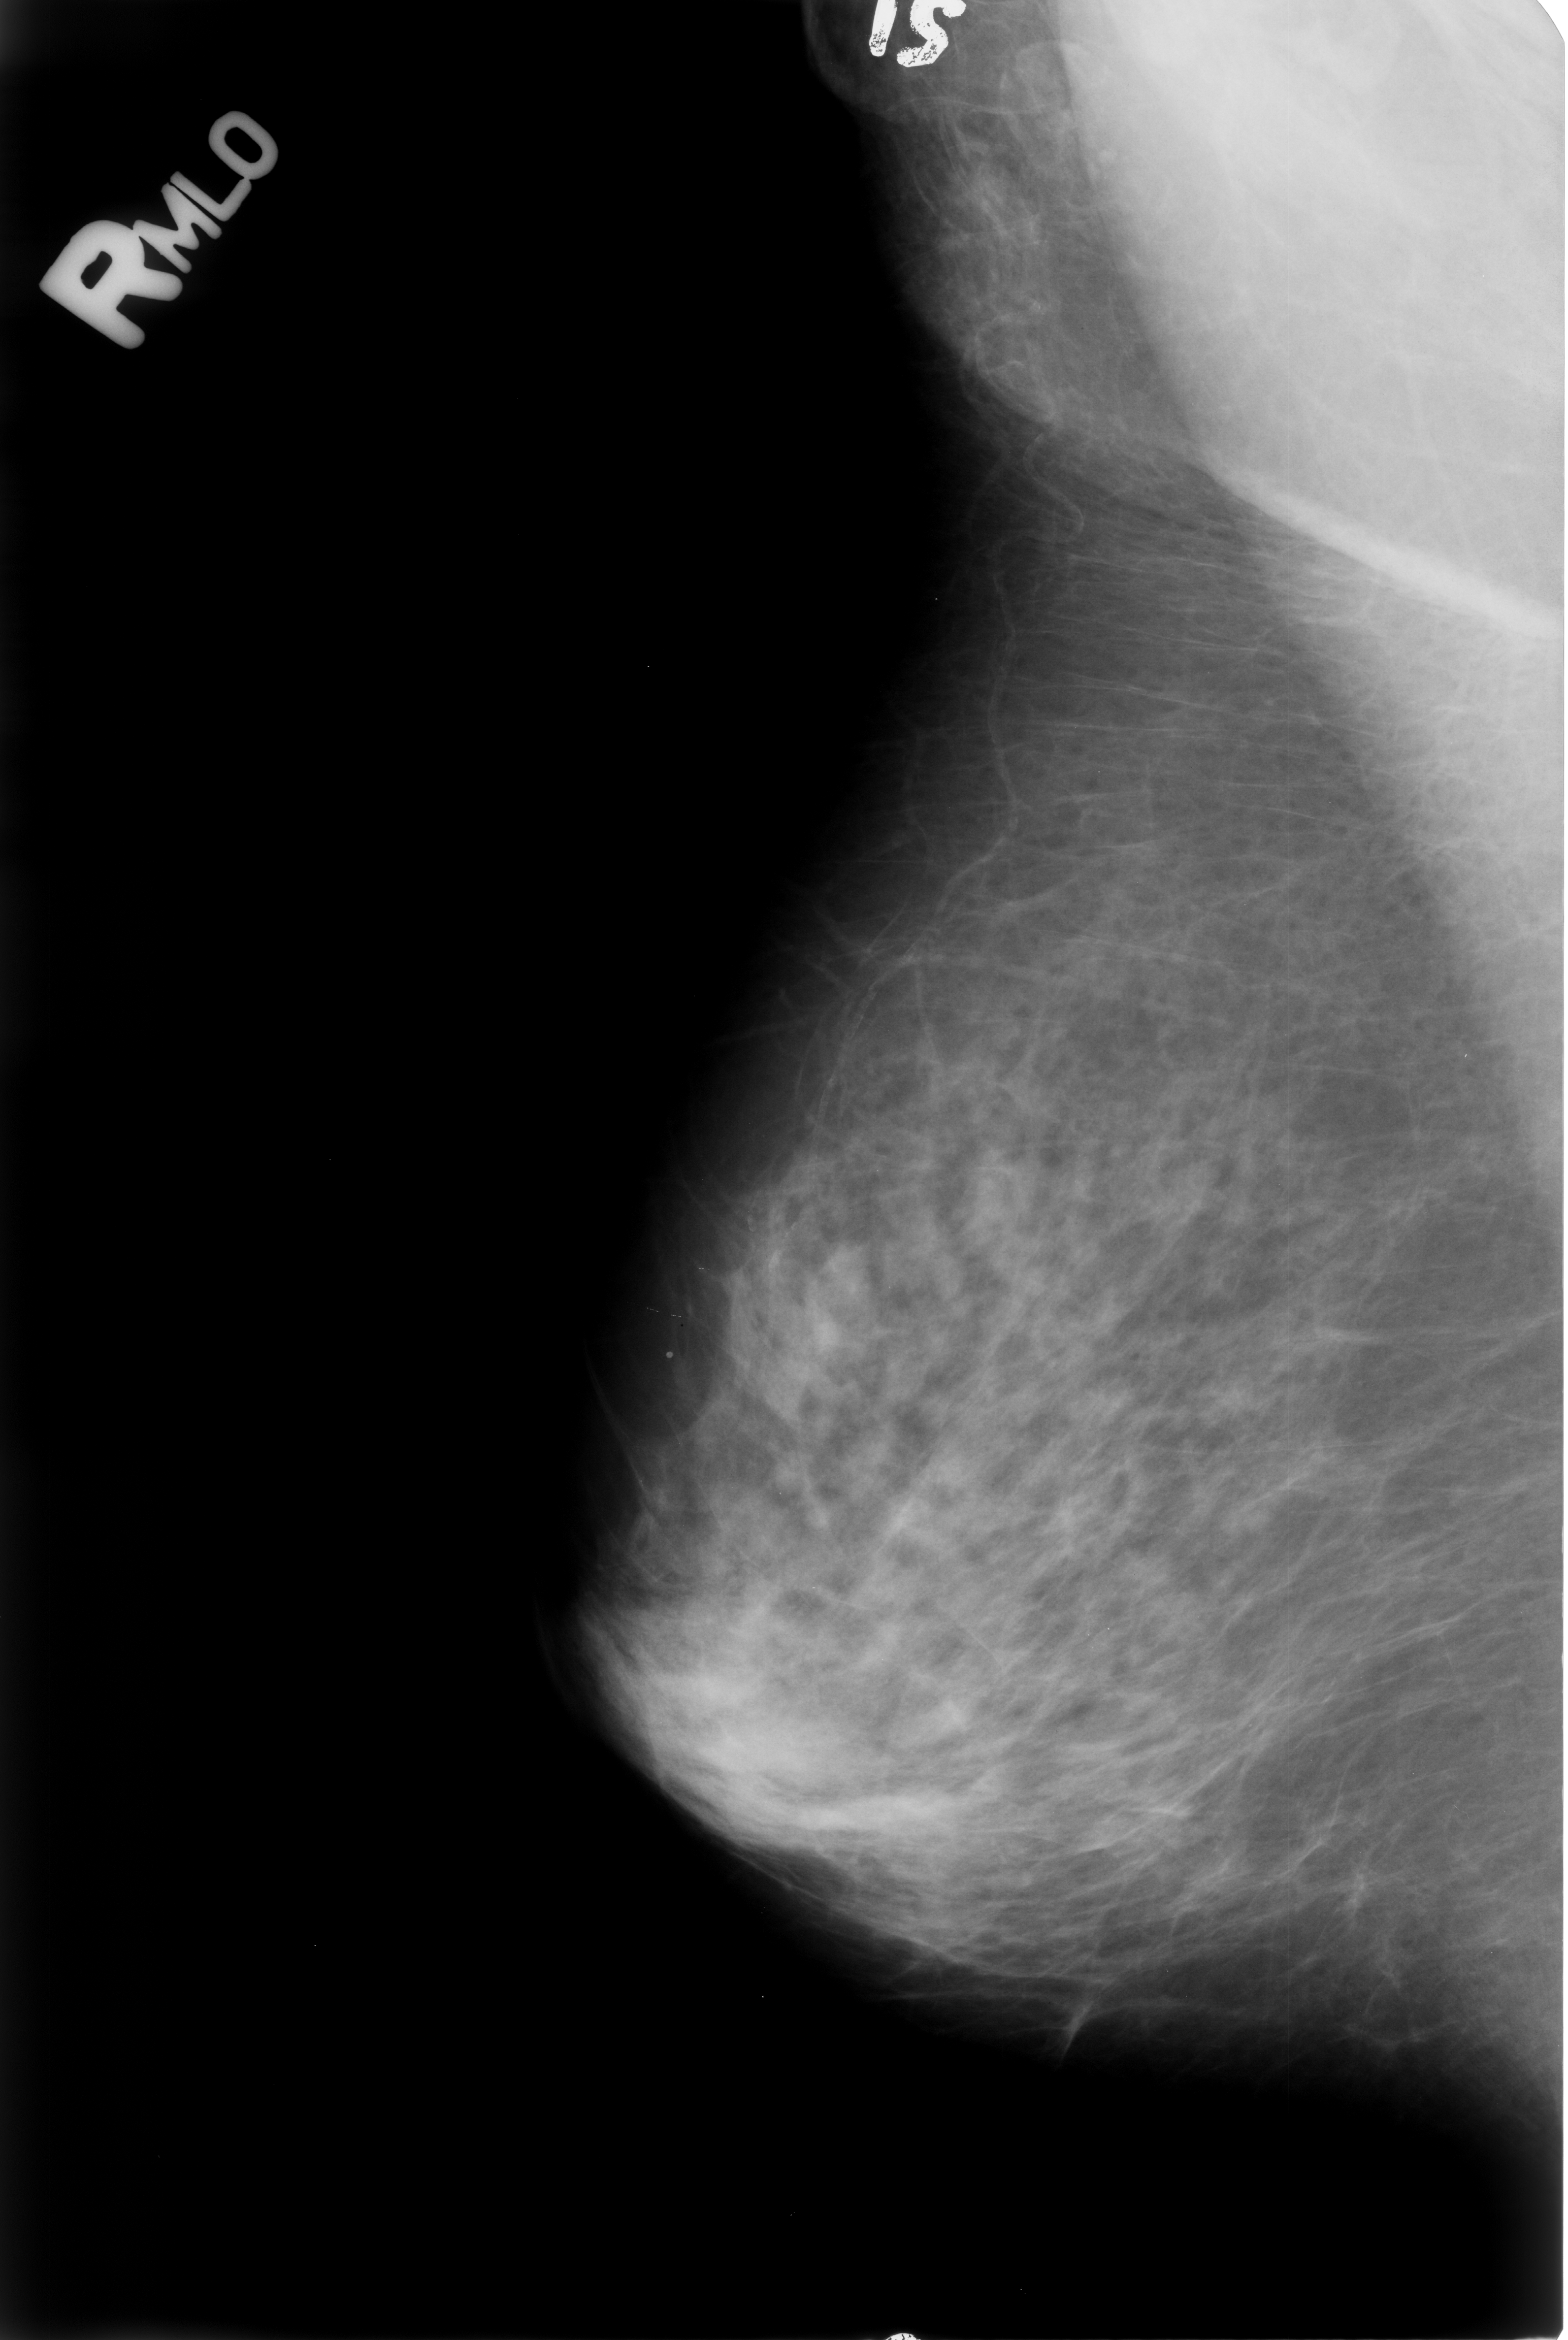
Digitized screen-film mammogram. Right breast. Mediolateral oblique (MLO) view. Breast composition: heterogeneously dense (BI-RADS density category 3 of 4). 1568 × 2340 image matrix.
Expert-marked regions of interest on this image (one box per marked abnormality):
- Finding 1 of 2: calcifications, morphology lucent center; BI-RADS assessment category 2; subtlety rating 3 on a 1 (subtle) to 5 (obvious) scale; outcome (as recorded, no biopsy): benign without callback (not worked up further): box from (x=654, y=1324) to (x=696, y=1374) px
- Finding 2 of 2: calcifications, morphology vascular; BI-RADS assessment category 2; subtlety rating 3 on a 1 (subtle) to 5 (obvious) scale; outcome (as recorded, no biopsy): benign without callback (not worked up further): (x=747, y=747)–(x=1065, y=1334)